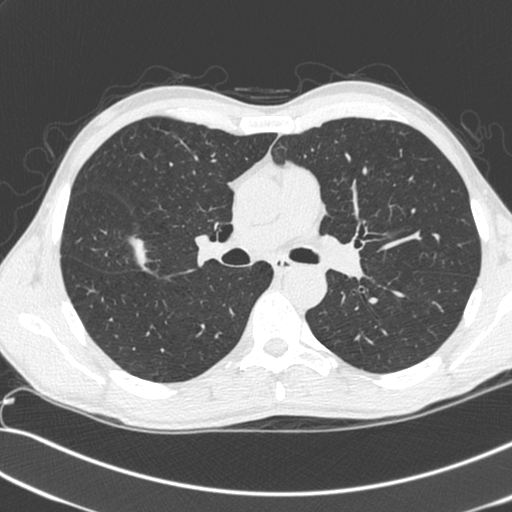
Chest CT (low-dose screening protocol), one axial image. Baseline screening round. Lung window (W 1500 / L -600 HU). 1.3 mm slice thickness. Slice 99 of 281 in the series. 512 × 512 image matrix. Male participant, aged 55 years at enrolment. Current smoker at enrolment.
- Lesion marked by an expert reader, box from (x=65, y=213) to (x=159, y=293) px.
- Screening reader's record for this exam (one nodule recorded; not confirmed to be the boxed lesion): non-calcified nodule or mass ≥4 mm, right upper lobe, 52 × 39 mm, spiculated (stellate) margins, soft tissue attenuation.
- Official screen result: positive, change unspecified: nodule(s) >= 4 mm or enlarging nodule(s), mass(es), or other non-specific abnormalities suspicious for lung cancer.